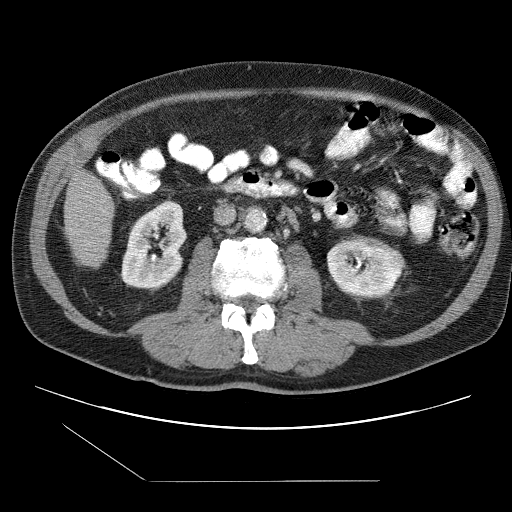
Contrast-enhanced abdominal CT (liver protocol), one axial slice; slice 16 of 109 in the series (ordered by position); reconstruction kernel STANDARD; one of 2 acquisitions stored at this slice position; soft-tissue window (W 400 / L 40 HU); 2.5 mm slice thickness; 512 × 512 image matrix, field of view 400 × 400 mm. Case-level facts recorded for this patient, not image findings: diagnosis: hepatocellular carcinoma (patient treated with transarterial chemoembolisation; whether this scan precedes or follows treatment is not stated here); TNM stage (as recorded): Stage-IIIB; Child-Pugh class: A; tumour differentiation: well differentiated; tumour nodularity: multinodular.
Outlined on this slice (semi-automatic segmentation, software-assisted and operator-edited):
- liver parenchyma outside the tumour (the mass and vessels are separate outlines, so this box may not span the whole liver): bounding box [x1, y1, x2, y2] px = [64, 170, 114, 266]